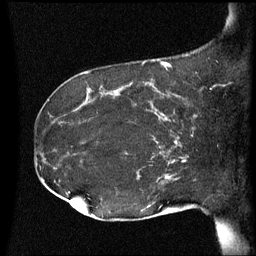
Breast MRI (dynamic contrast-enhanced), one sagittal slice. Dynamic contrast-enhanced series, image 2 of 3 at this slice position (ordered by acquisition). 1.5 T. TE 4.2 ms, TR 8.4 ms. 2.5 mm slice thickness. 256 × 256 image matrix. Female patient, age 41 years. From the clinical record (not read from this slice): setting: breast cancer imaged before/during neoadjuvant chemotherapy; receptor status: HER2-positive.
Annotated regions visible in this slice (semi-automatic segmentation, software-assisted and operator-edited):
- analysis volume of interest (the breast-tissue region the enhancement analysis was run in; not a lesion): box from (x=122, y=84) to (x=195, y=137) px
- tumour enhancement mask (voxels above the 70 % enhancement threshold inside the analysis volume of interest): (x=145, y=84)–(x=195, y=137)